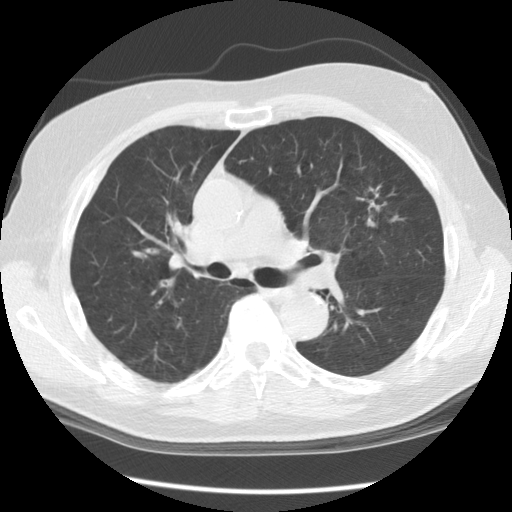
Chest CT (low-dose screening protocol), one axial image, second screening round (one year after baseline), lung window (W 1500 / L -600 HU), 2.5 mm slice thickness, standard (soft-tissue) reconstruction kernel (STANDARD), slice 85 of 140 in the series. Male, age 70 years at enrolment. Current smoker at enrolment.
Expert reader's lesion annotation, bounding box [x1, y1, x2, y2] px = [341, 180, 401, 235]. The screening reader recorded 3 non-calcified nodules or masses ≥4 mm on this exam; which of them this box marks is not recorded. Lung cancer was diagnosed 396 days after this screen (after the third annual screen): adenocarcinoma, NOS, left upper lobe, moderately differentiated (G2), stage IIIA (AJCC 6th edition), 17 mm at pathology.